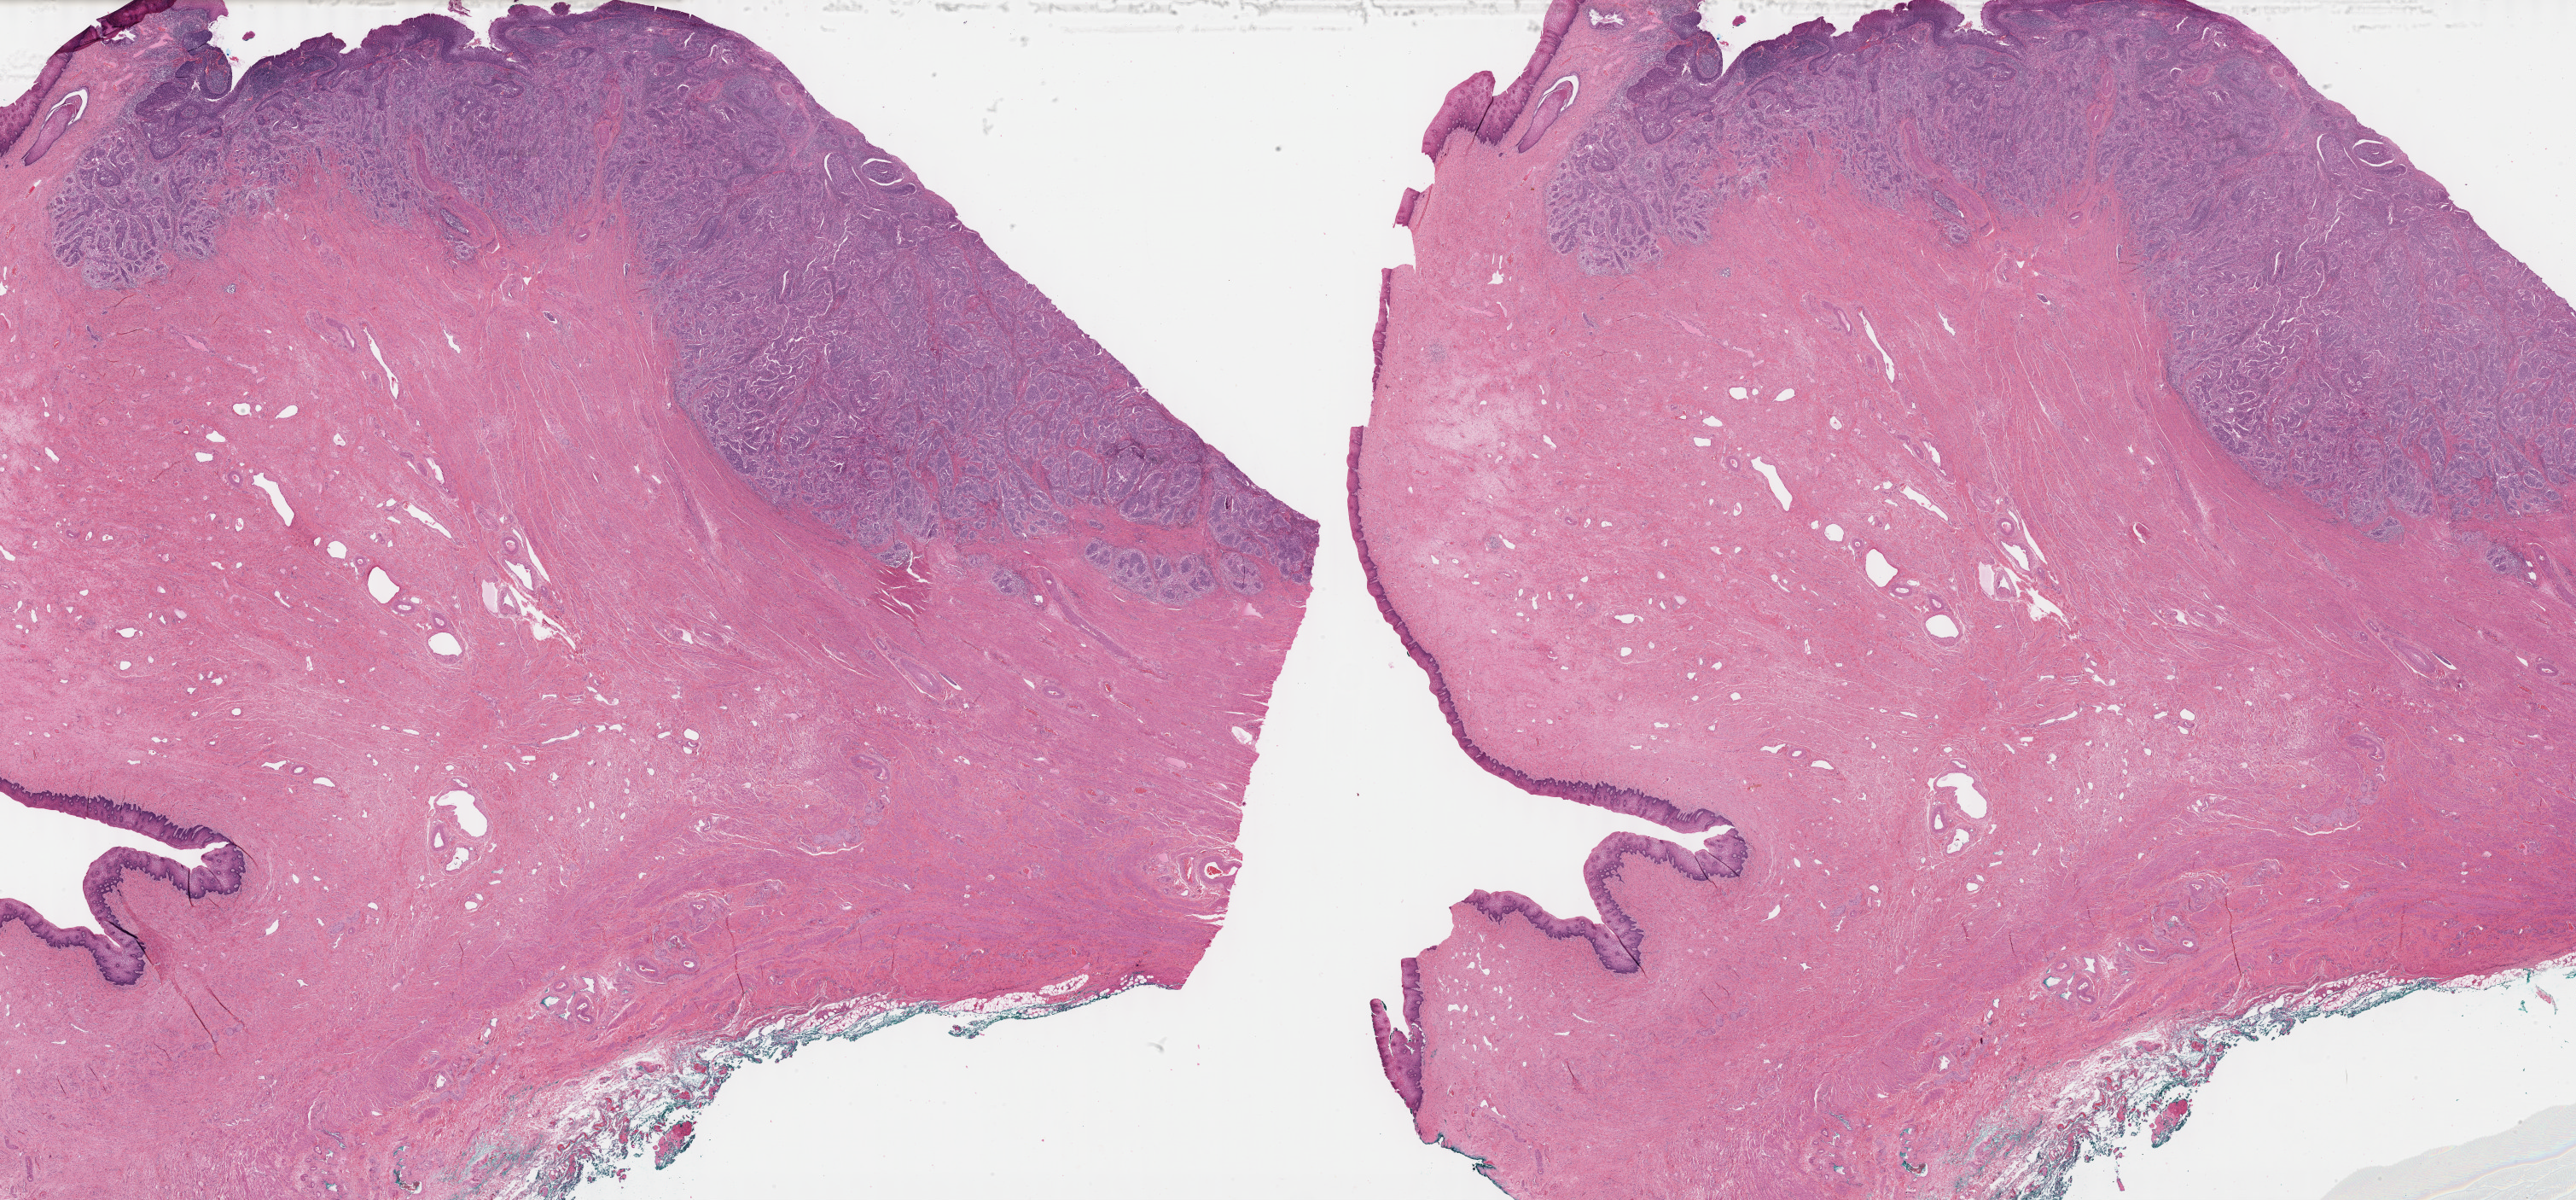
Digitized Hematoxylin and eosin (H&E) stained tissue section (whole slide) — a low-resolution overview of the entire scanned area, about 48.8 x 22.7 mm (slide scanned at 40x), FFPE section, cervix, primary tumour sample. Female, age 41 years at initial diagnosis.
Pathologic diagnosis: Squamous cell carcinoma, large cell, nonkeratinizing, NOS (cervix uteri).